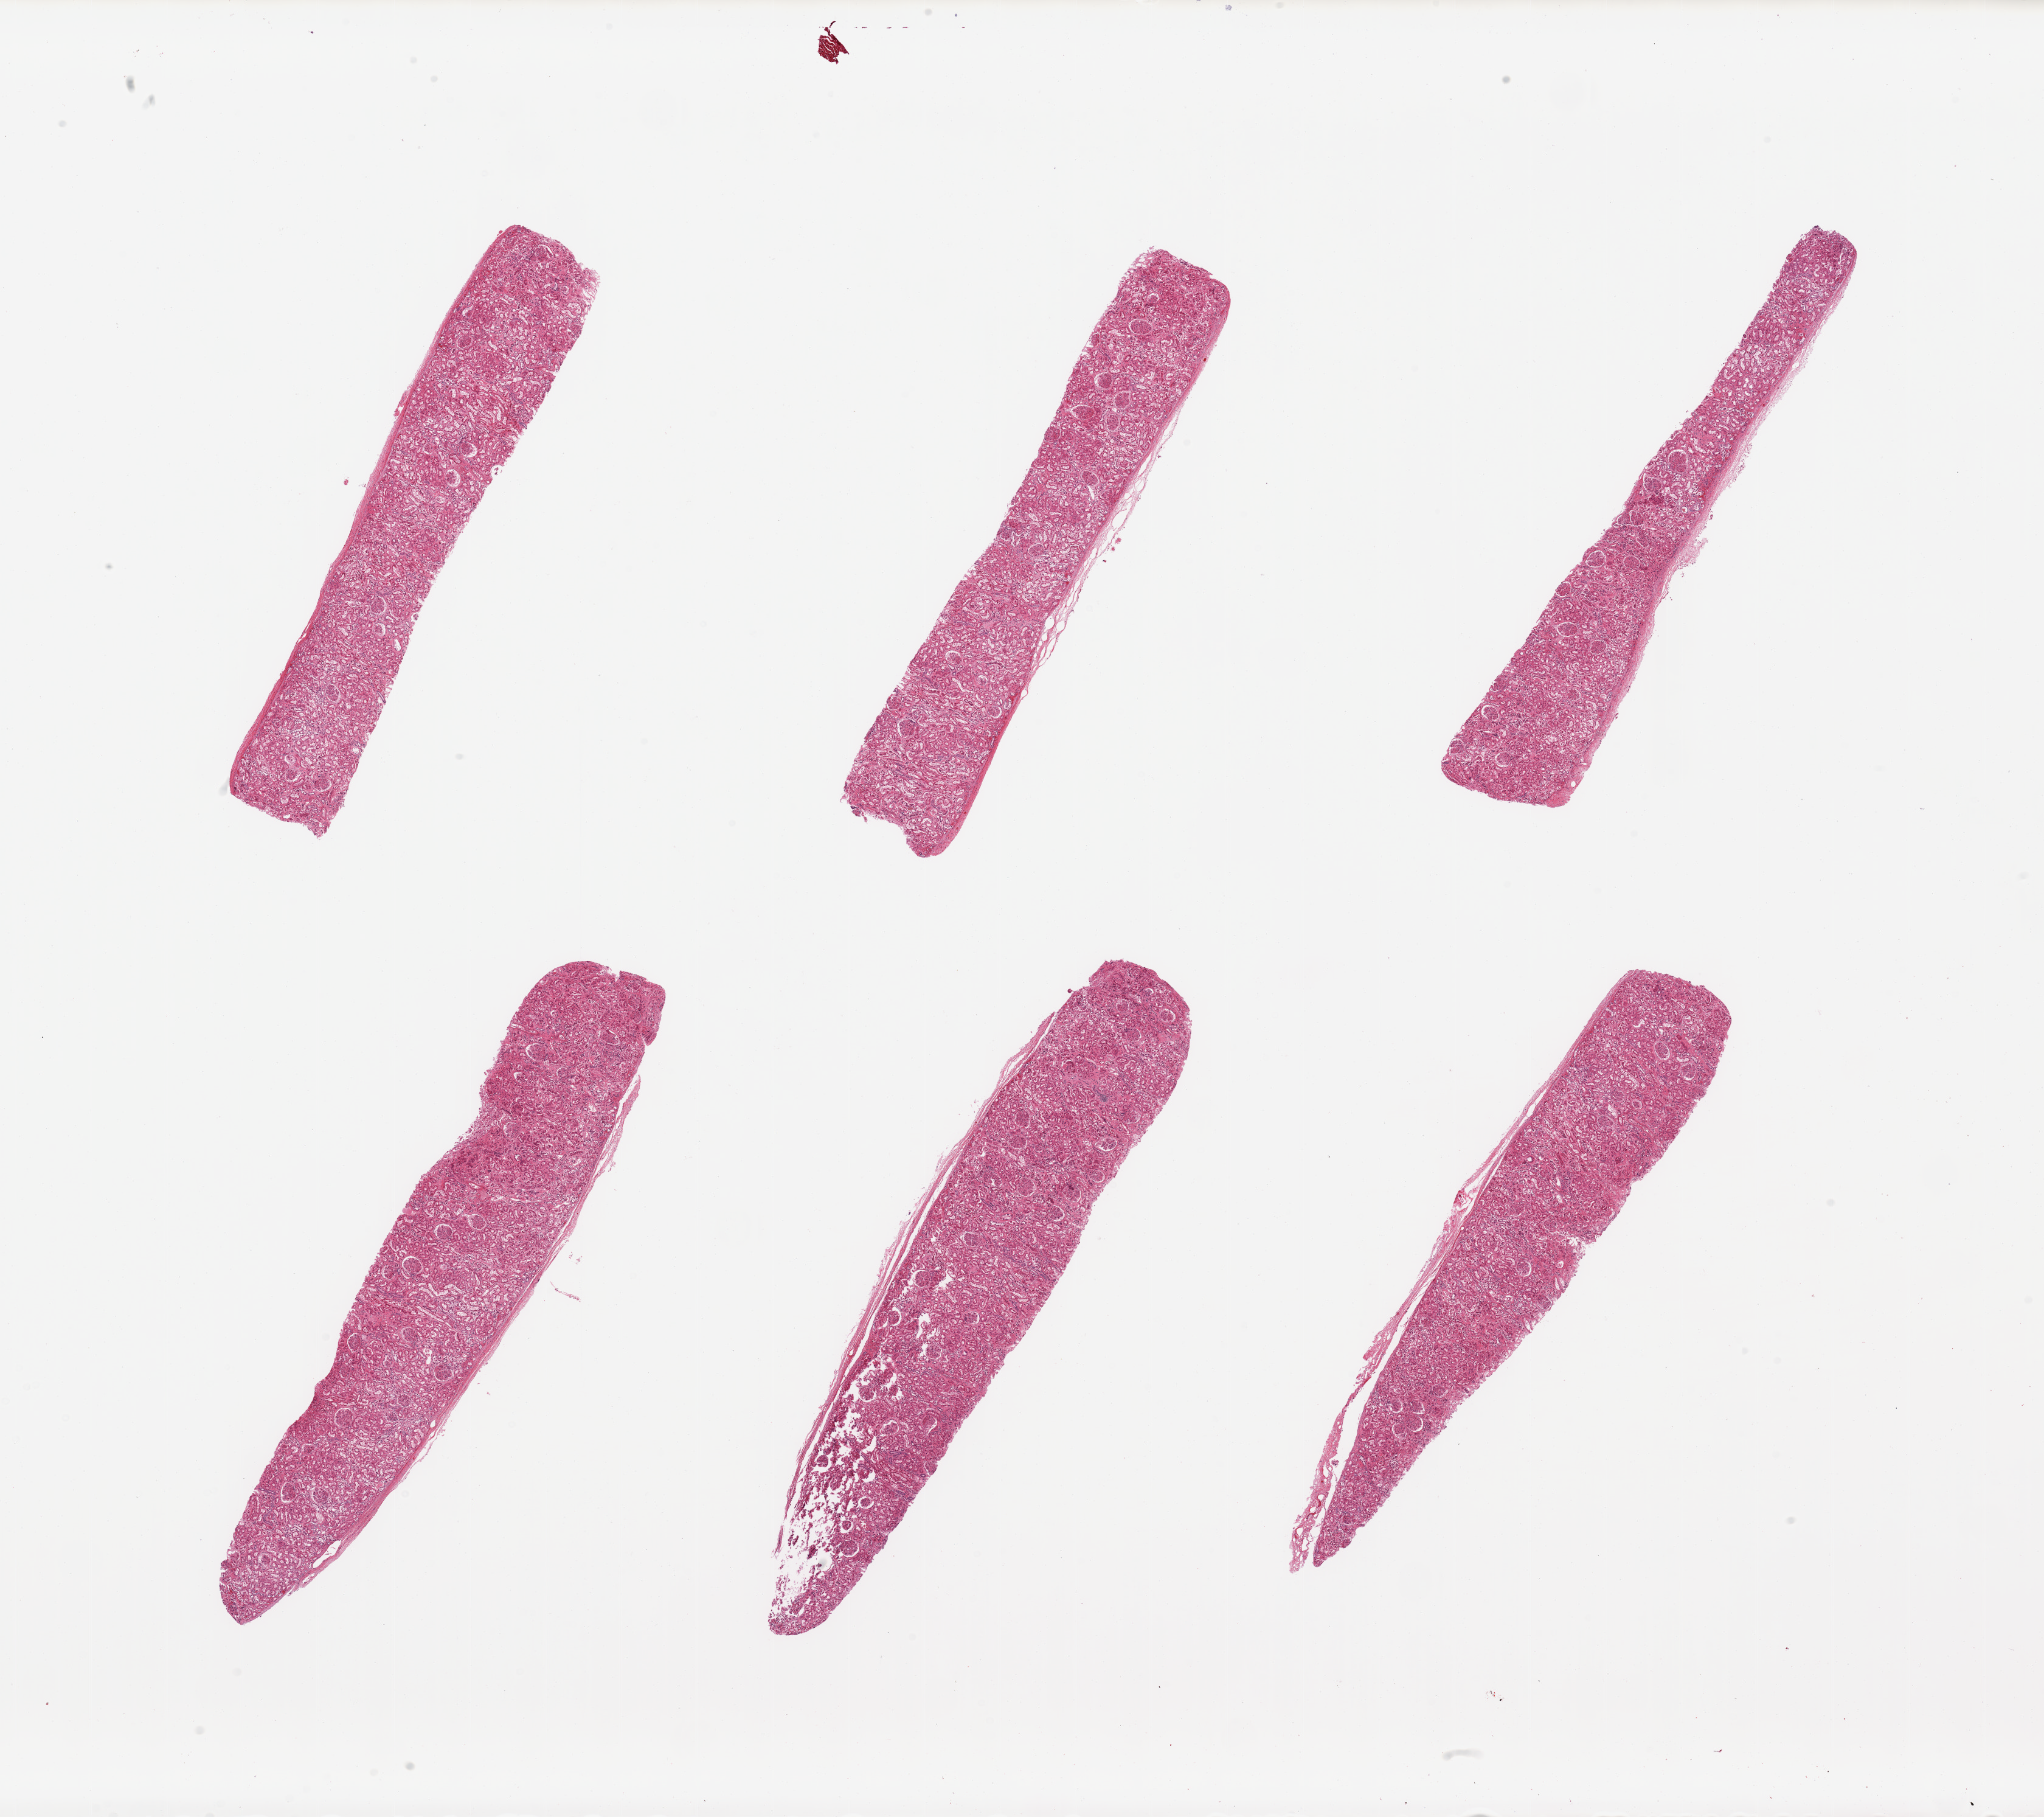
Hematoxylin and eosin (H&E) whole-slide image — a low-resolution overview of the entire scanned area, about 26.6 x 23.6 mm. PAXgene-fixed paraffin-embedded (PFPE) section. Sampled site (target tissue): renal cortex. Tissue donor sample. Donor sex: male.
Reviewer comment on this tissue sample: 6 pieces; no active or chronic lesions.